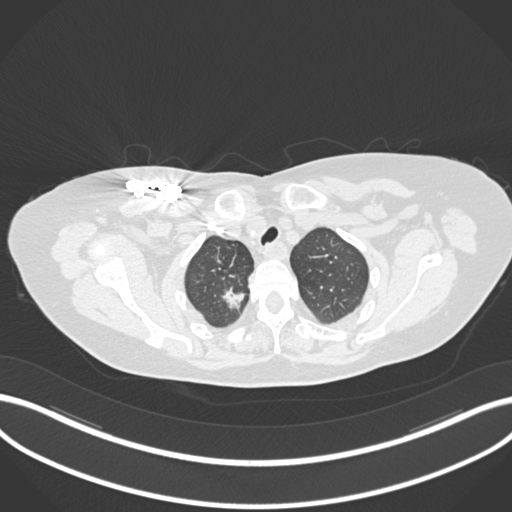
Chest CT, one axial slice. Position 155 of 176 along the scan axis. 120 kVp. Lung window (W 1500 / L -600 HU). 1 mm slice thickness. 512 × 512 image matrix, field of view 400 × 400 mm. Female patient, age 72 years. From the clinical record (not read from this slice): clinical TNM (as recorded): T1c N0 M0.
Annotated regions visible in this slice (rectangle marked by the reading radiologist):
- lung tumour (recorded histology: adenocarcinoma): box from (x=223, y=282) to (x=249, y=316) px